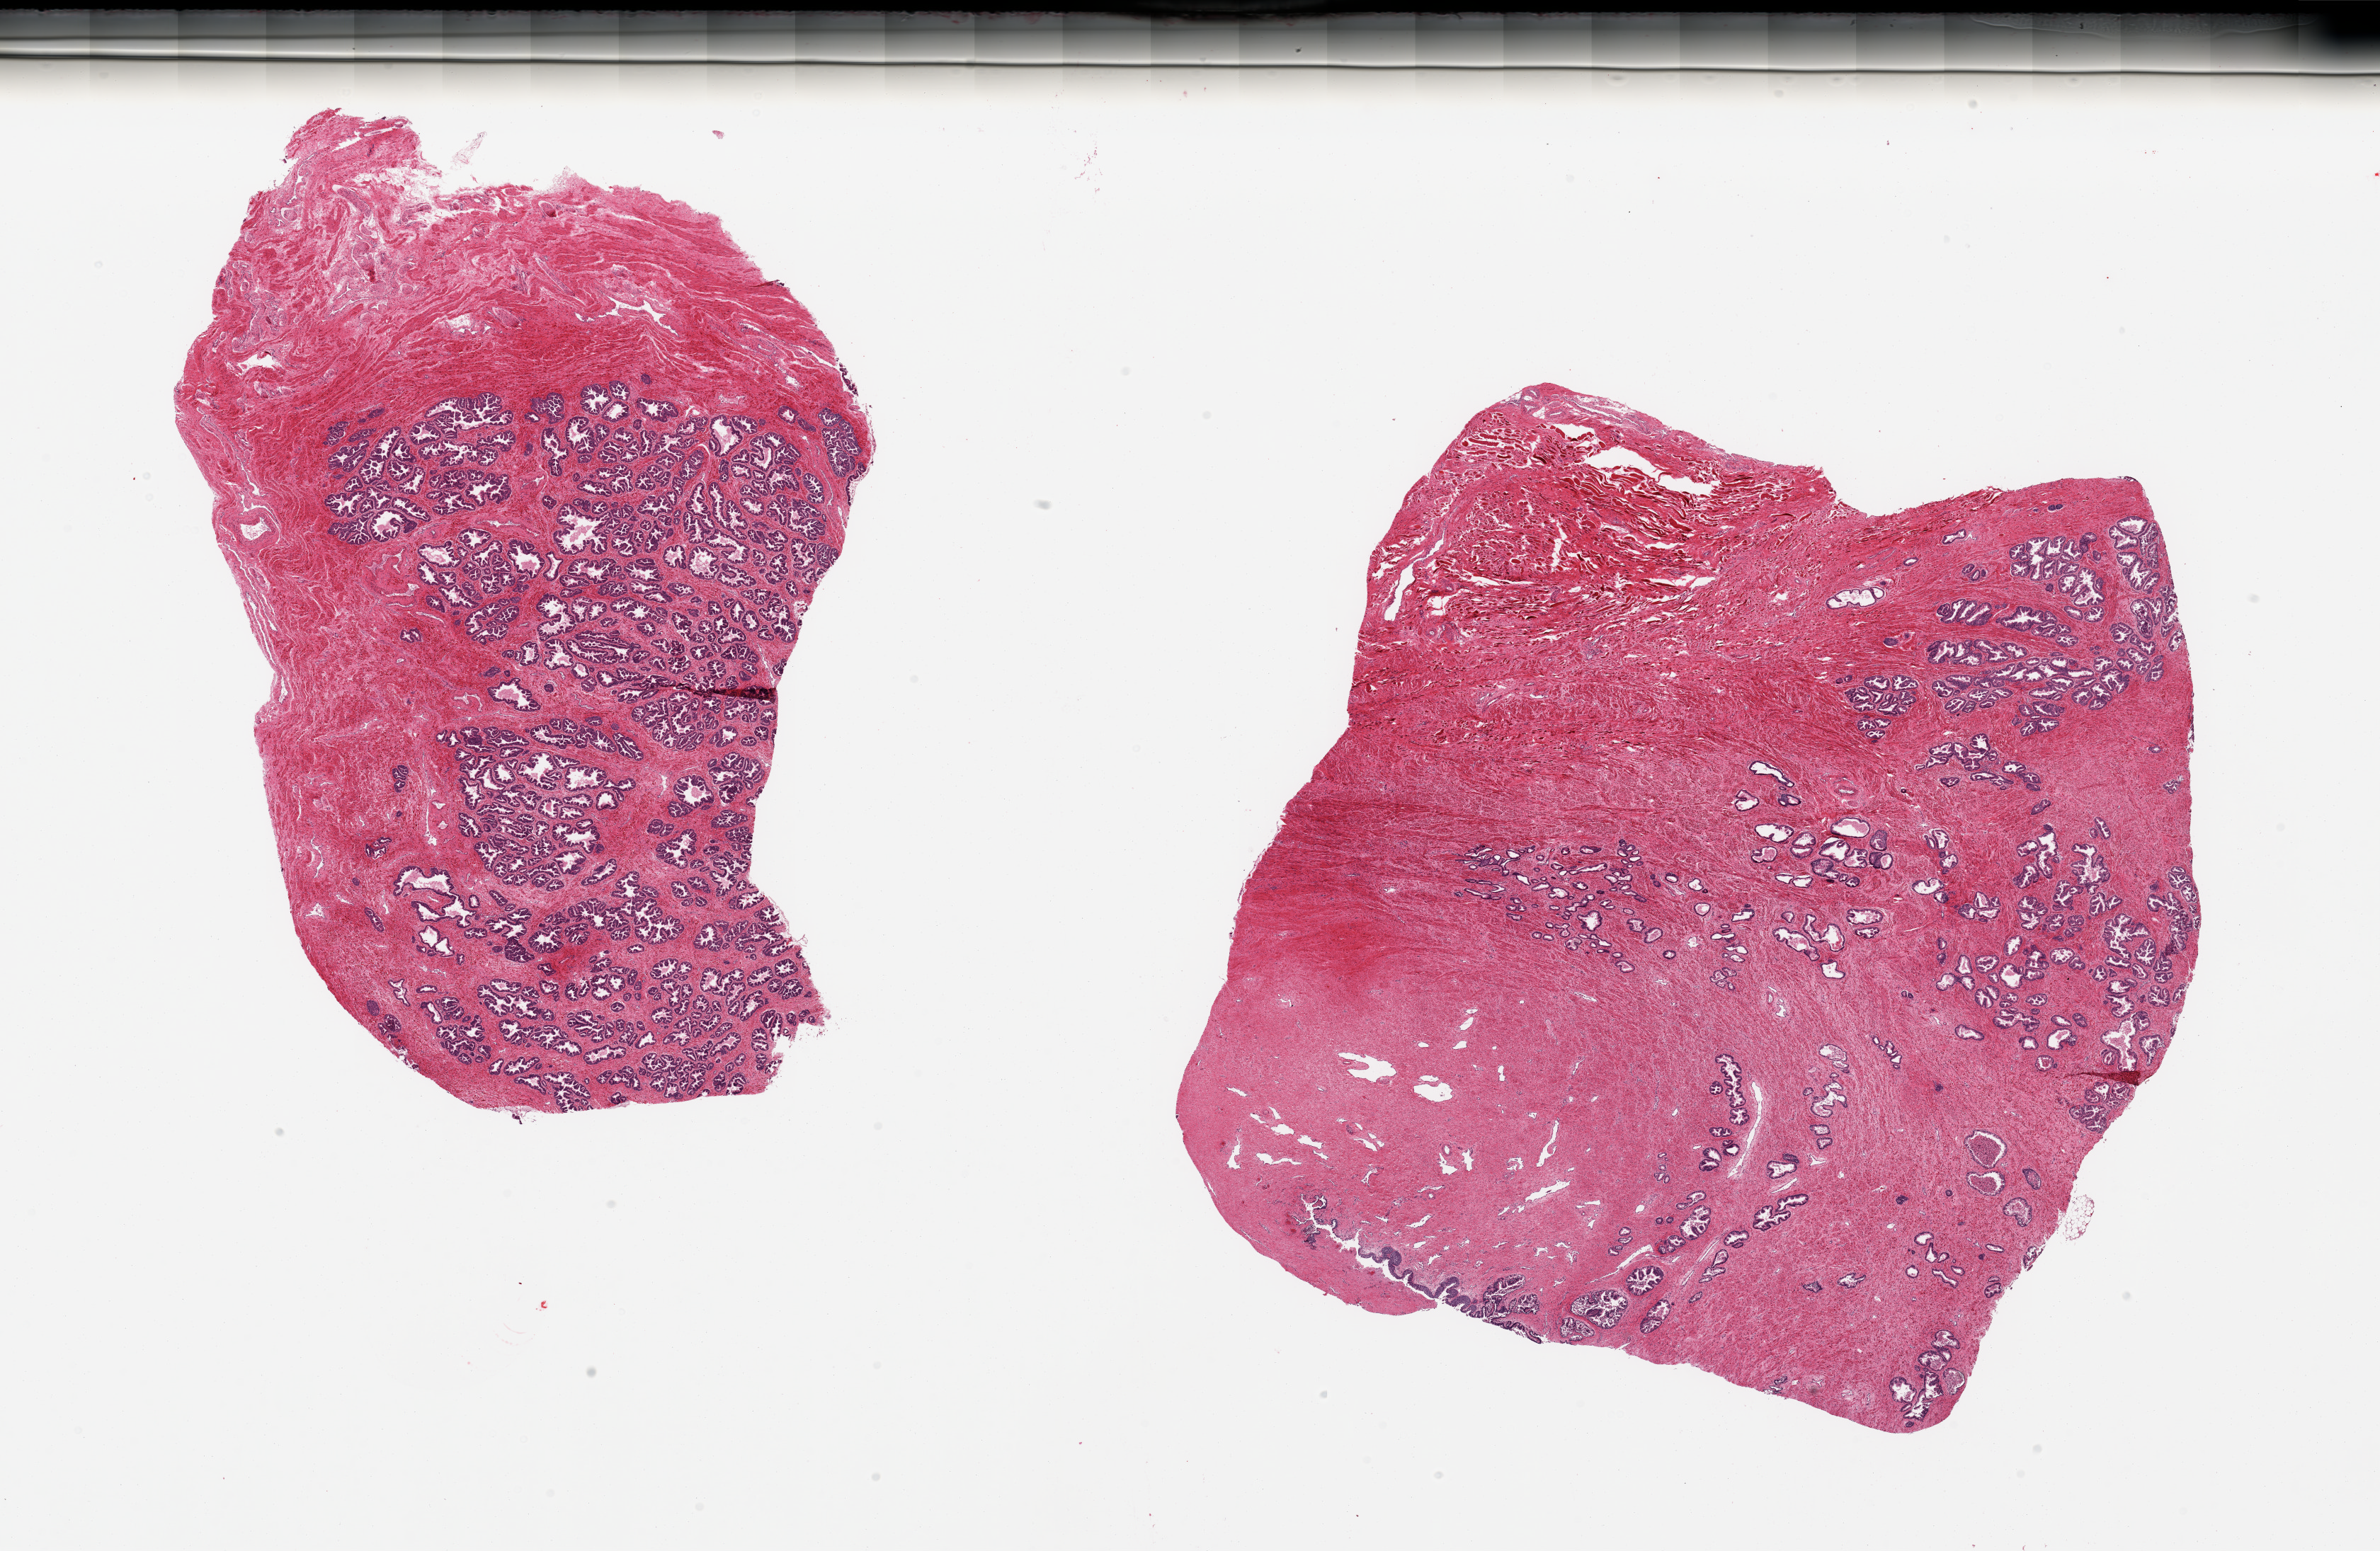
Digitized H&E-stained section, brightfield — whole scanned area (about 26.6 x 17.3 mm, slide scanned at 20x) shown as a low-resolution overview, PAXgene-fixed, paraffin-embedded tissue, sampled site (target tissue): prostate, tissue donor sample. Male donor.
• pathologist's review note for this sample: 2 pieces; fibromuscular stroma and glands, 1 piece includes portion of urethra and skeletal muscle fibers